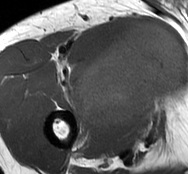
MRI of an extremity soft-tissue mass, one axial slice. Slice 55 of 93 in the series (ordered by position). MR volume resampled by the dataset authors to the PET/CT grid (not the native acquisition matrix). 188 × 174 image matrix, field of view 184 × 170 mm. Male patient. Case-level facts recorded for this patient, not image findings: histological type: undifferentiated - pleiomorphic; grade: high; site of the primary tumour: right thigh.
Structures marked on this image (expert contour drawn on MRI and transferred to this co-registered scan by the dataset authors):
- gross tumour volume including surrounding oedema: box from (x=75, y=21) to (x=185, y=129) px
- gross tumour volume (mass): (x=75, y=21)–(x=185, y=129)